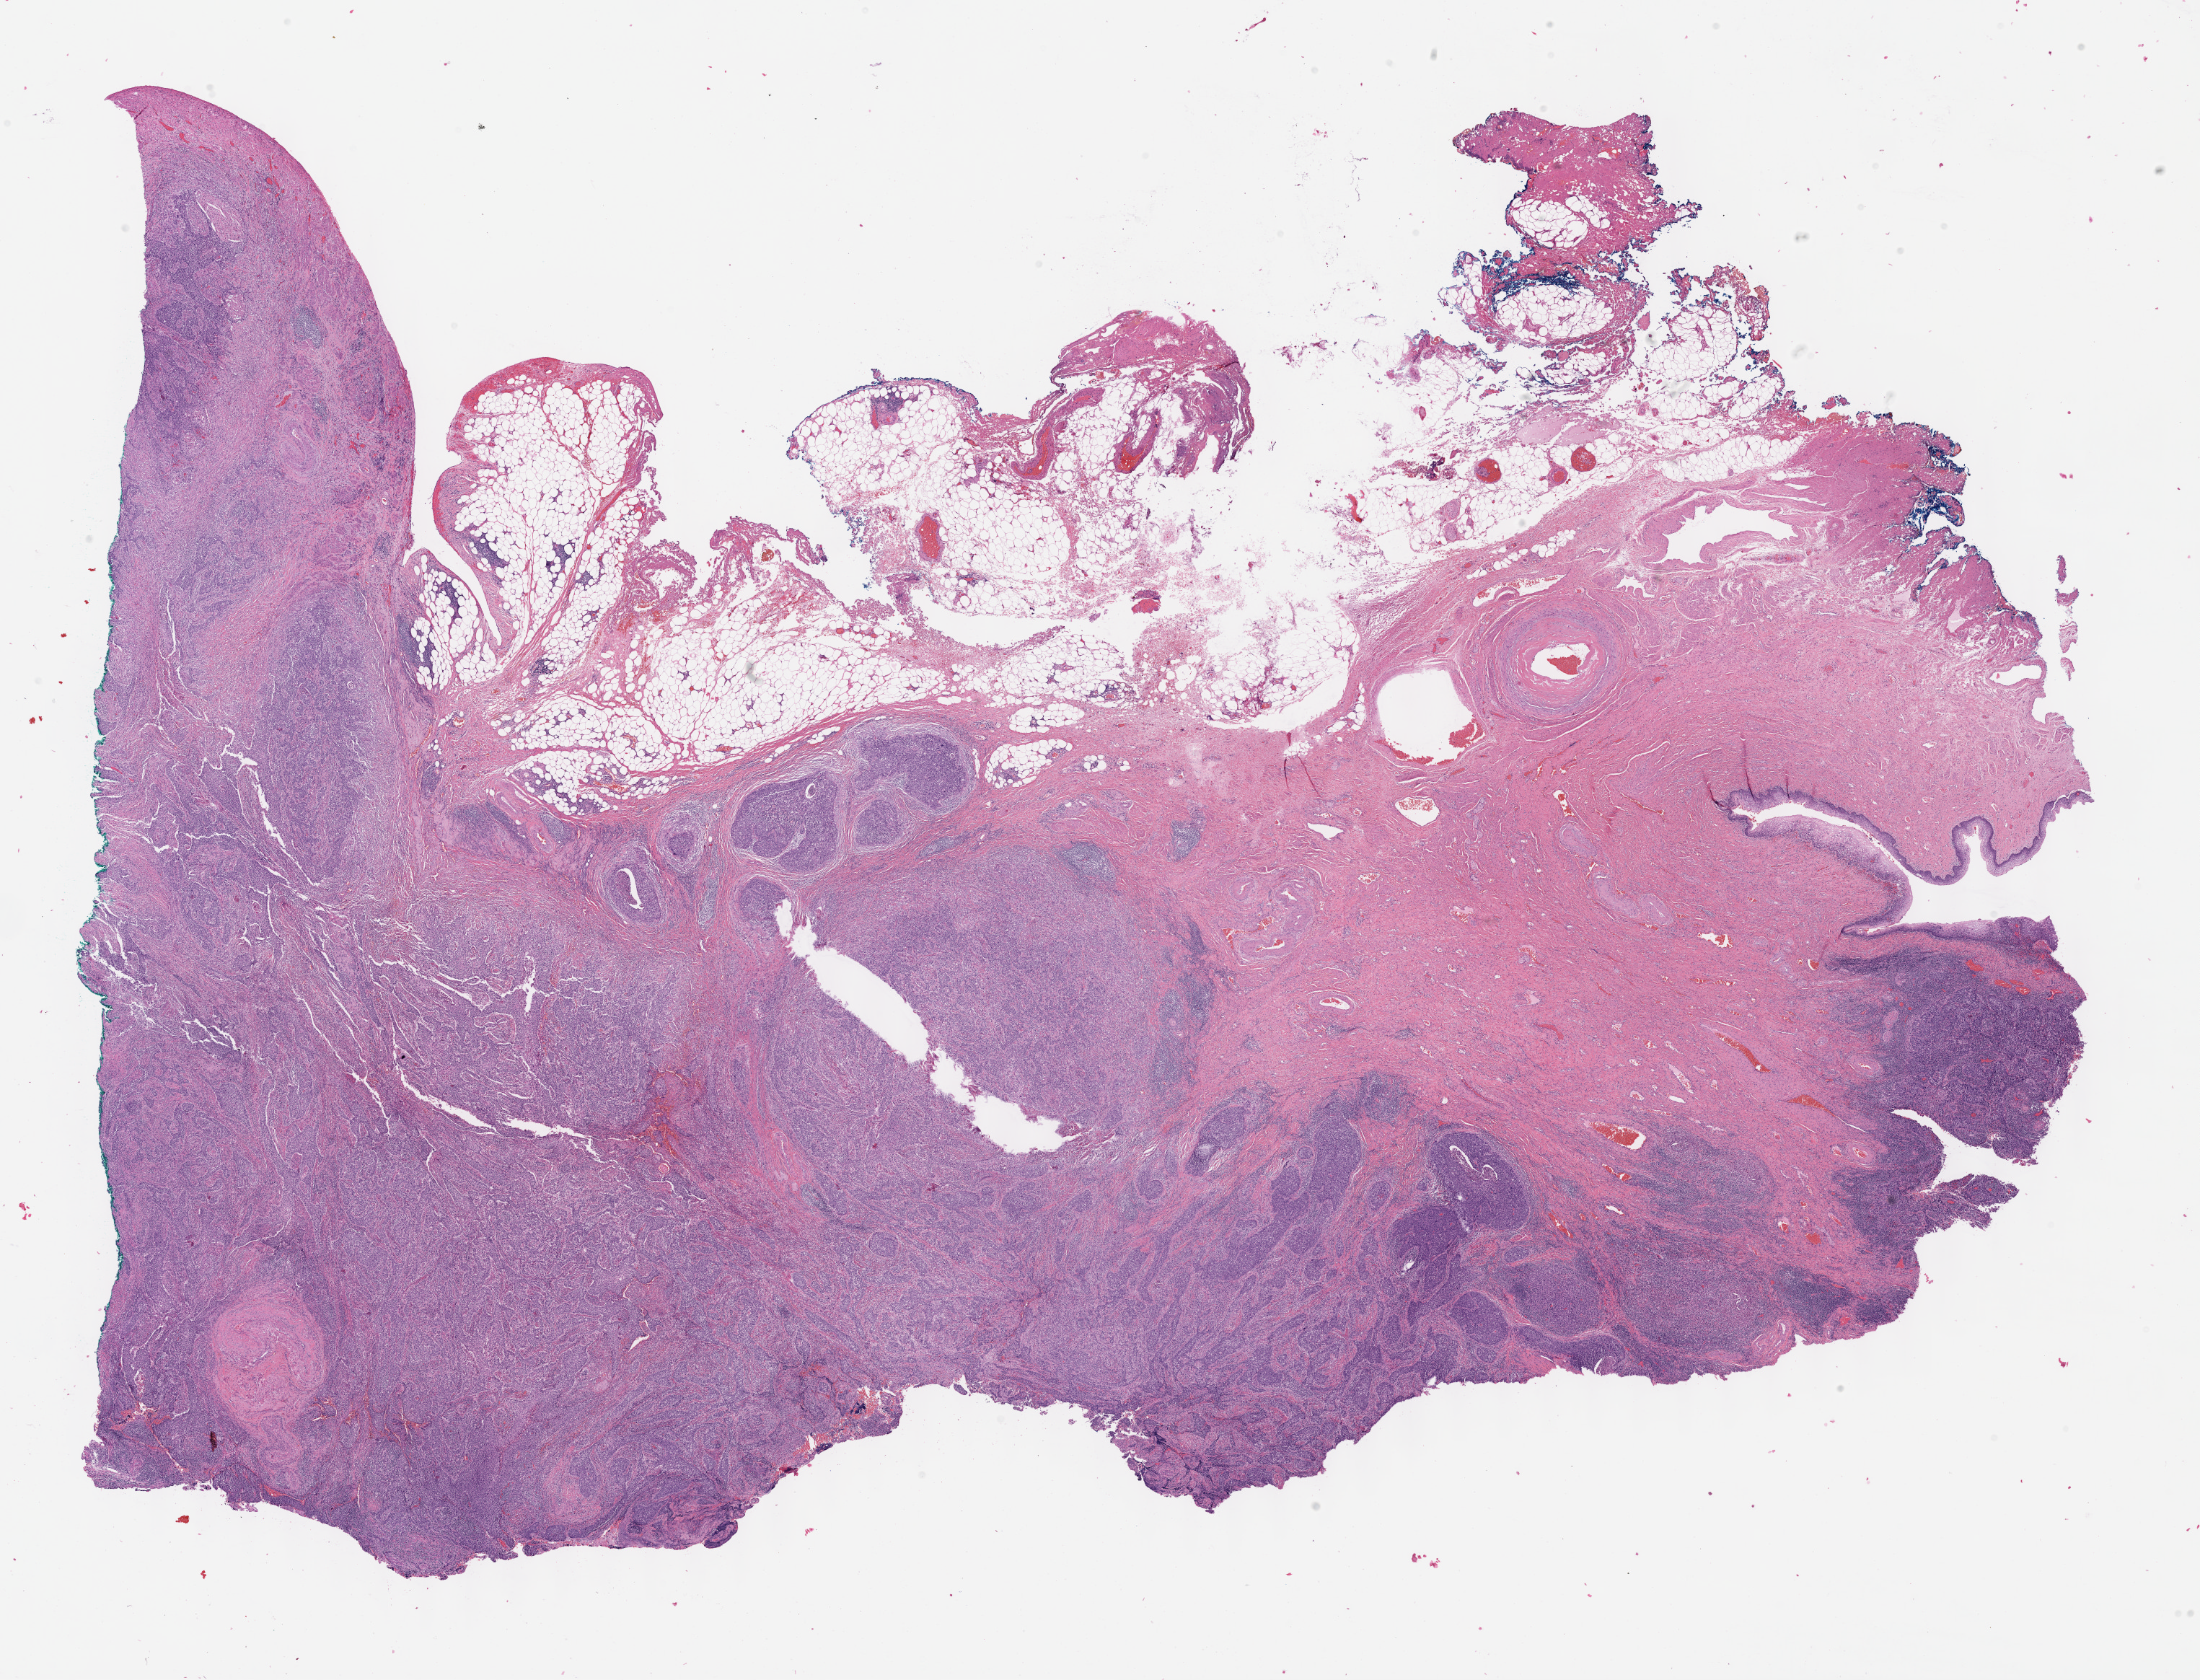
Digitized Hematoxylin and eosin (H&E) stained tissue section (whole slide), shown as a low-resolution overview of the whole scanned area (about 24.6 x 18.8 mm, from a 40x scan); FFPE section; sample: primary tumour, cervix. Female, age 54 years at initial diagnosis. Histologic grade: G3 (poorly differentiated).
FIGO stage: IB1. Pathologic diagnosis: Squamous cell carcinoma, NOS (cervix uteri).